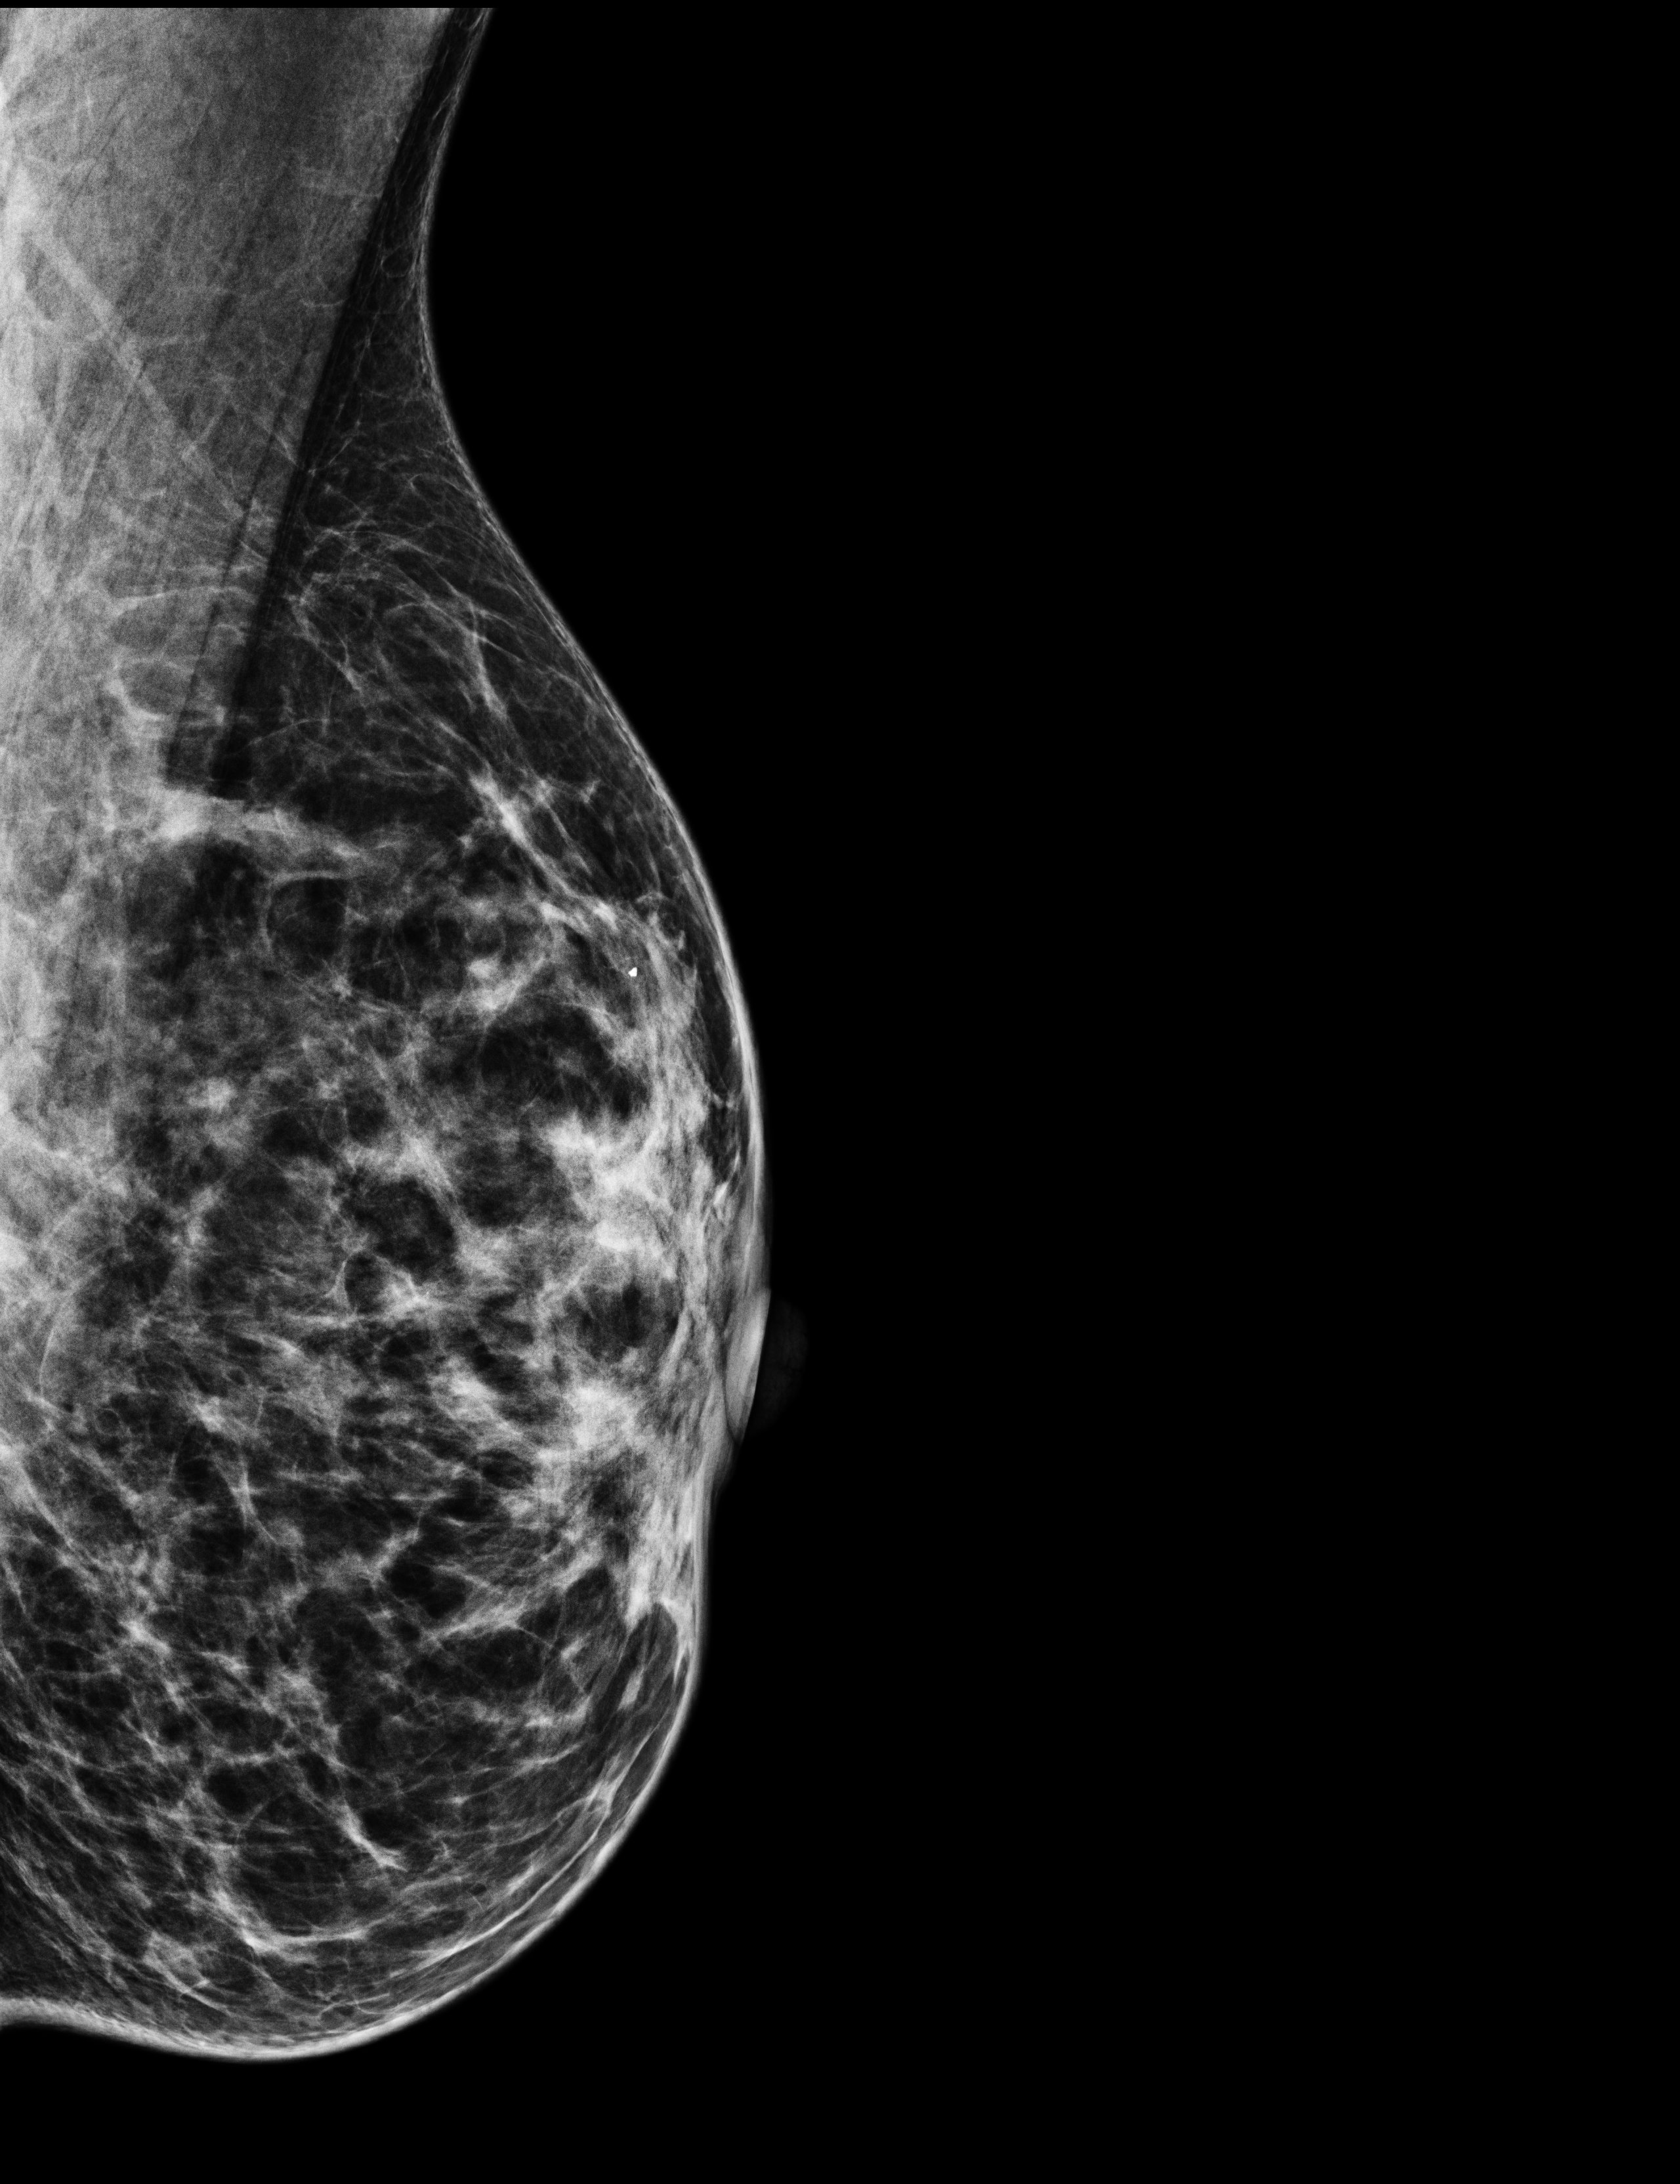
Digital mammogram (FFDM); left breast; medio-lateral oblique projection; annual screening mammography examination; compressed breast thickness 47 mm; system: Selenia Dimensions. Patient aged 43 years (female).
- breast density at the screening exam (both breasts): heterogeneously dense (BI-RADS density category c)
- final BI-RADS assessment for this screening round (tomosynthesis exam, both breasts): category 2
- recall: no recall after this screen